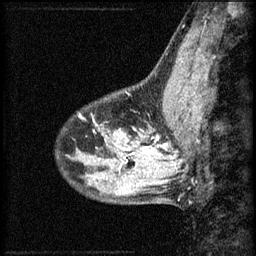
Breast MRI (dynamic contrast-enhanced), one sagittal slice. Slice 17 of 60 in the series (ordered by position). 3 images stored at this slice position (order not interpretable as contrast timing). 1.5 T. TE 4.2 ms, TR 8.2 ms. 256 × 256 image matrix. Female patient, age 40 years.
Structures marked on this image (semi-automatically segmented with operator editing):
- analysis volume of interest (the breast-tissue region the enhancement analysis was run in; not a lesion): box from (x=108, y=108) to (x=167, y=159) px
- tumour enhancement mask (voxels above the 70 % enhancement threshold inside the analysis volume of interest): (x=116, y=138)–(x=165, y=159)